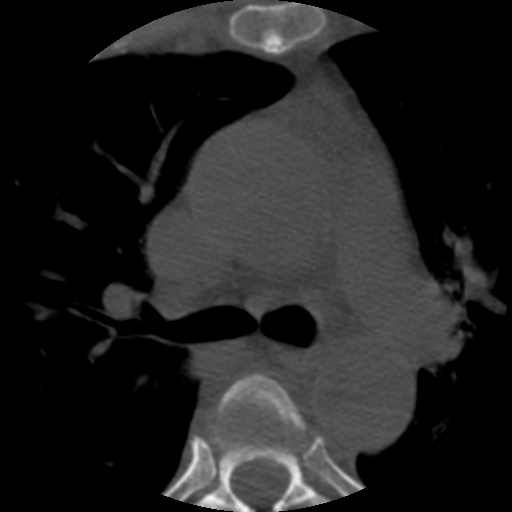
CT including the spine, one axial slice; slice 383 of 508 in the series (ordered by position); reconstruction kernel STANDARD; 120 kVp; bone window (W 1800 / L 400 HU); 512 × 512 image matrix, field of view 160 × 160 mm. Patient age 57 years. From the clinical record (not read from this slice): primary cancer: prostate.
Structures marked on this image (semi-automatically segmented with operator editing):
- T4 vertebra: box from (x=211, y=375) to (x=306, y=444) px
- T5 vertebra: (x=198, y=374)–(x=324, y=512)